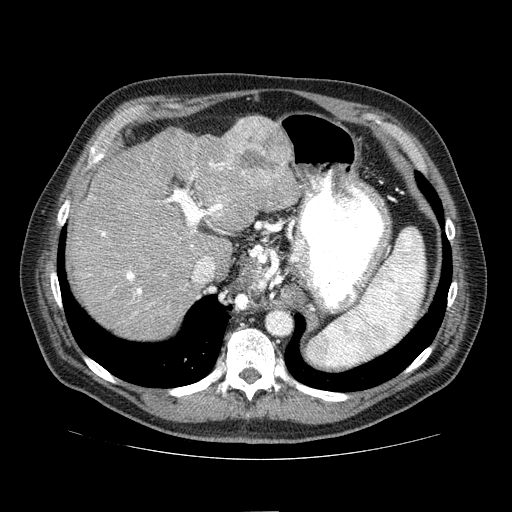
Contrast-enhanced abdominal CT (liver protocol), one axial slice; position 54 of 81 along the scan axis; reconstruction kernel STANDARD; 100 kVp; one of 2 acquisitions stored at this slice position; soft-tissue window (W 400 / L 40 HU); 2.5 mm slice thickness; 512 × 512 image matrix. From the clinical record (not read from this slice): diagnosis: hepatocellular carcinoma (patient treated with transarterial chemoembolisation; whether this scan precedes or follows treatment is not stated here); TNM stage (as recorded): Stage-IIIA; Child-Pugh class: A; tumour differentiation: well differentiated; tumour nodularity: multinodular.
Structures marked on this image (semi-automatically segmented with operator editing):
- abdominal aorta: box from (x=268, y=312) to (x=291, y=334) px
- liver parenchyma outside the tumour (the mass and vessels are separate outlines, so this box may not span the whole liver): (x=68, y=116)–(x=300, y=338)
- mass: (x=221, y=116)–(x=290, y=187)
- liver vessels: (x=88, y=161)–(x=228, y=315)